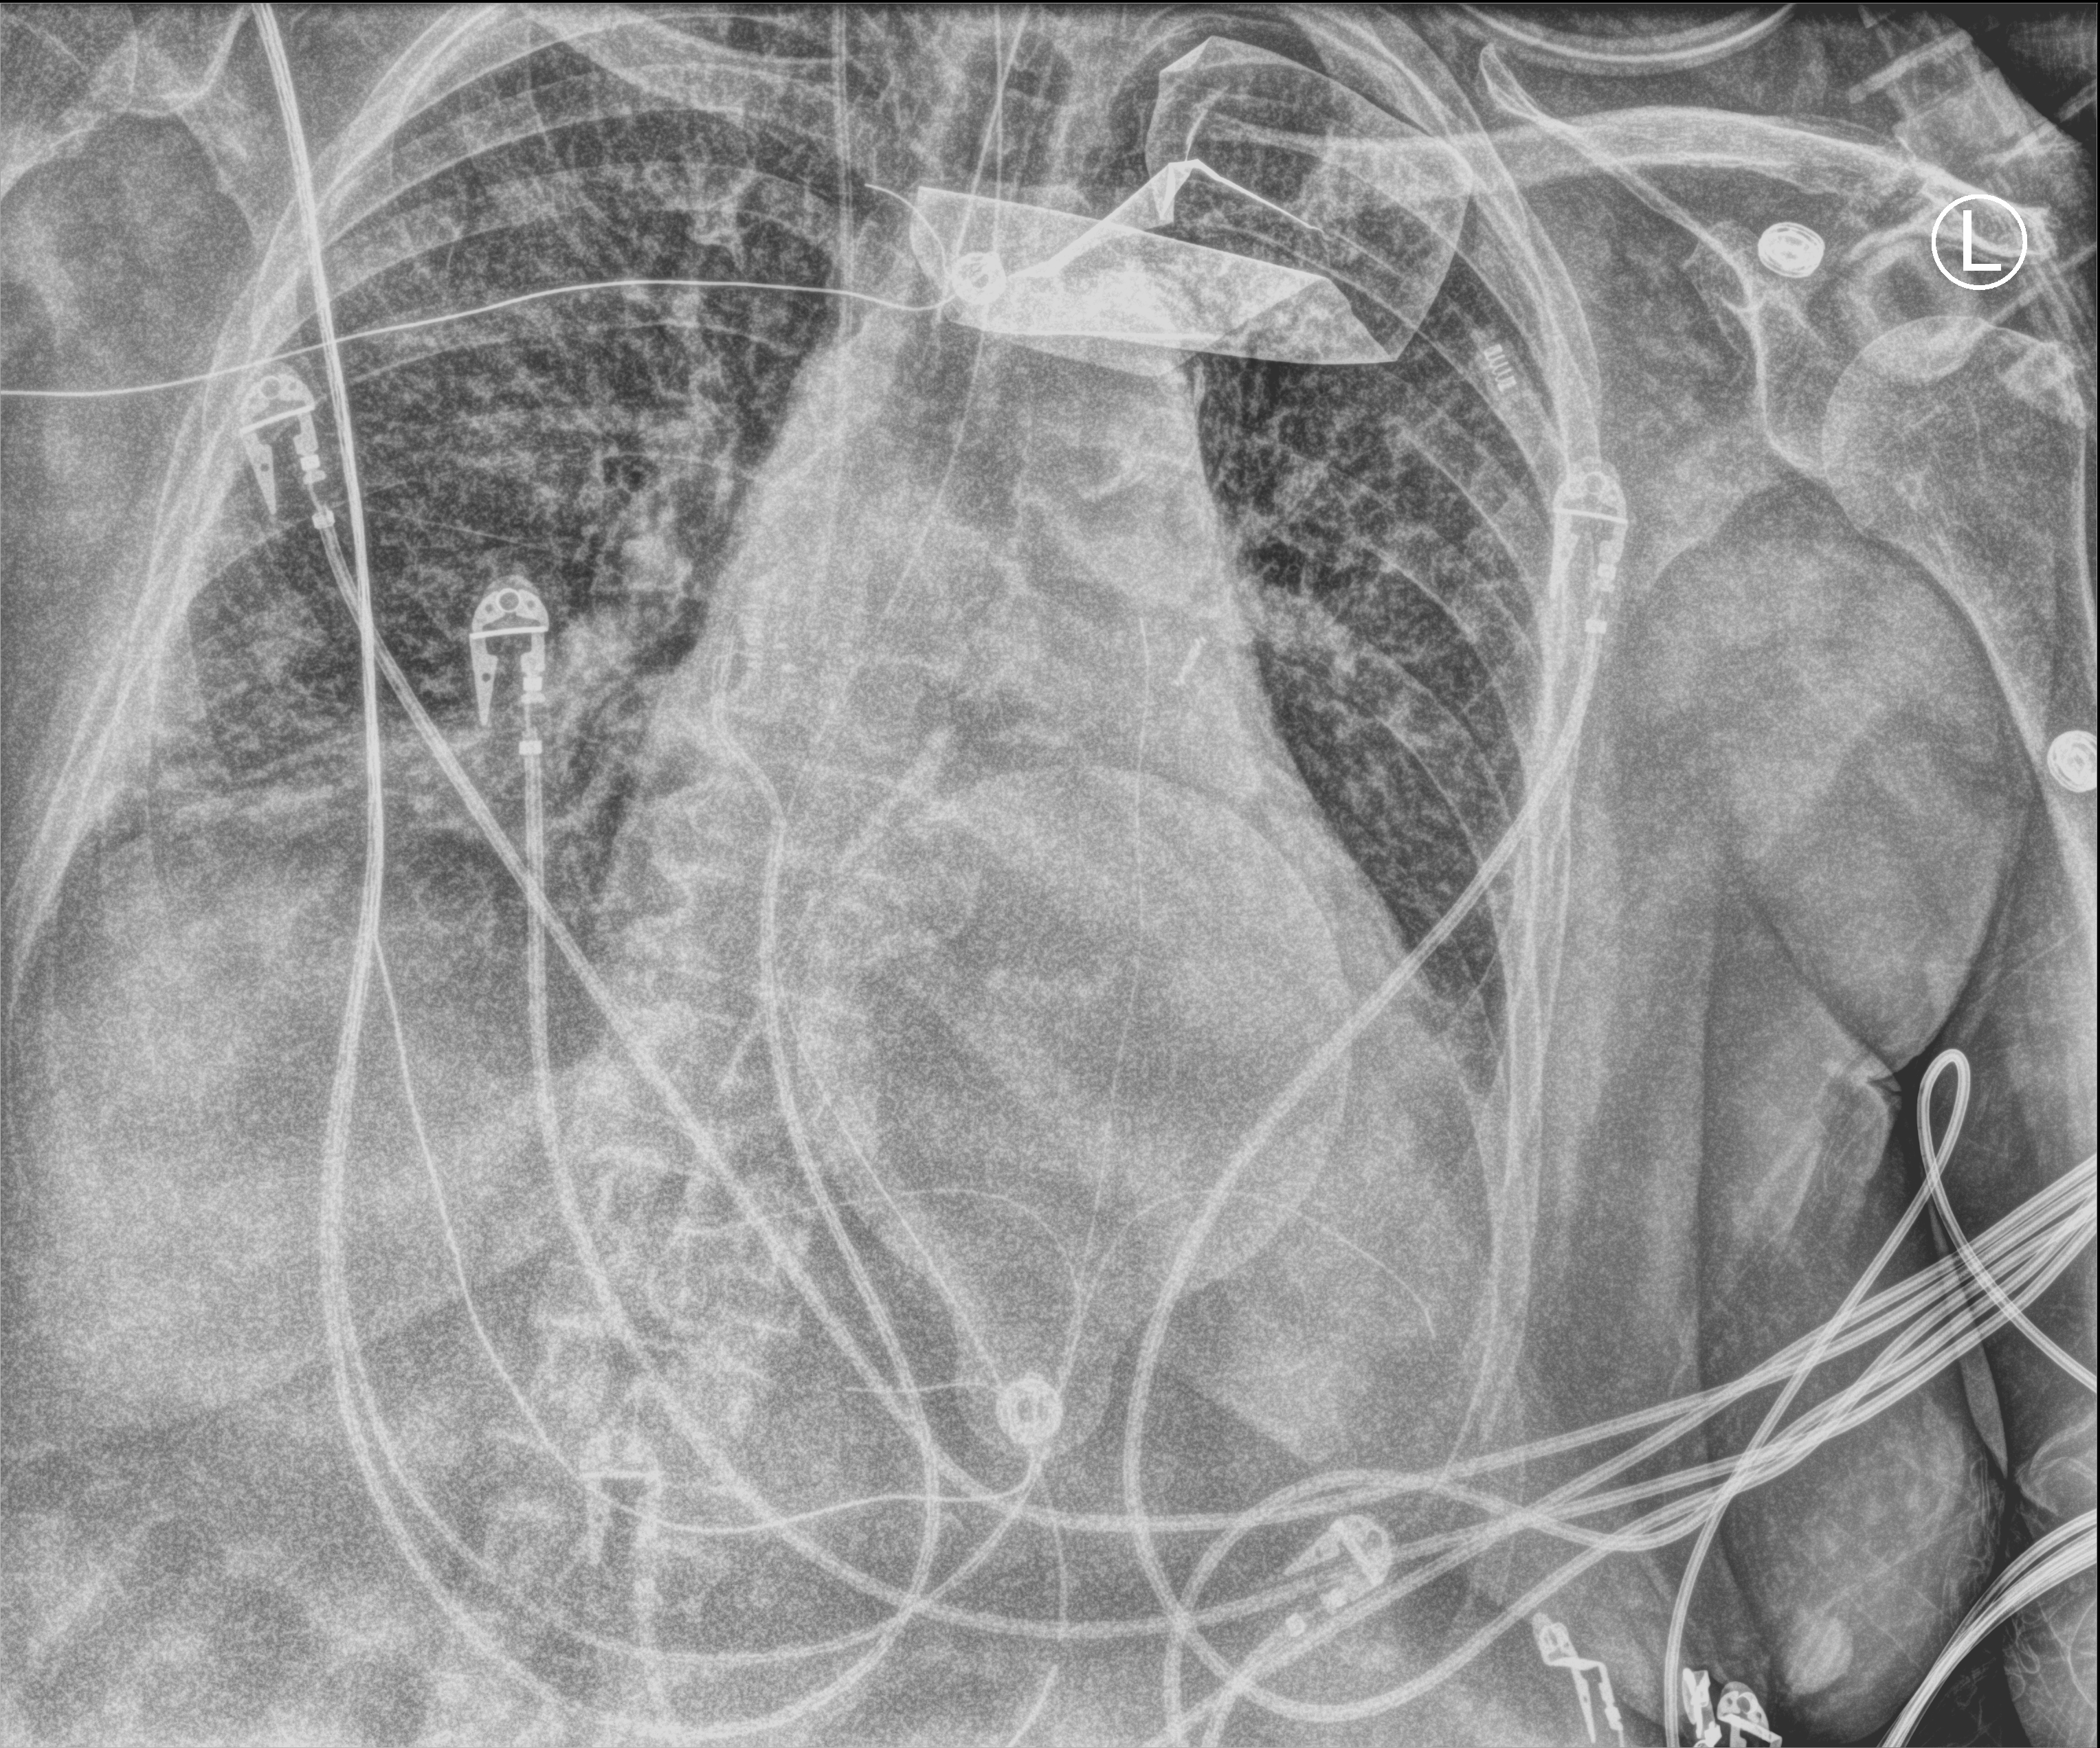
Chest X-ray (portable); anteroposterior (AP) projection. Patient hospitalised with COVID-19; female, aged 75–90 years.
From the hospital-stay record, not from the radiograph (when in the stay this image was taken is not recorded): length of hospital stay: 10 days; other chronic lung disease (admission record): no.